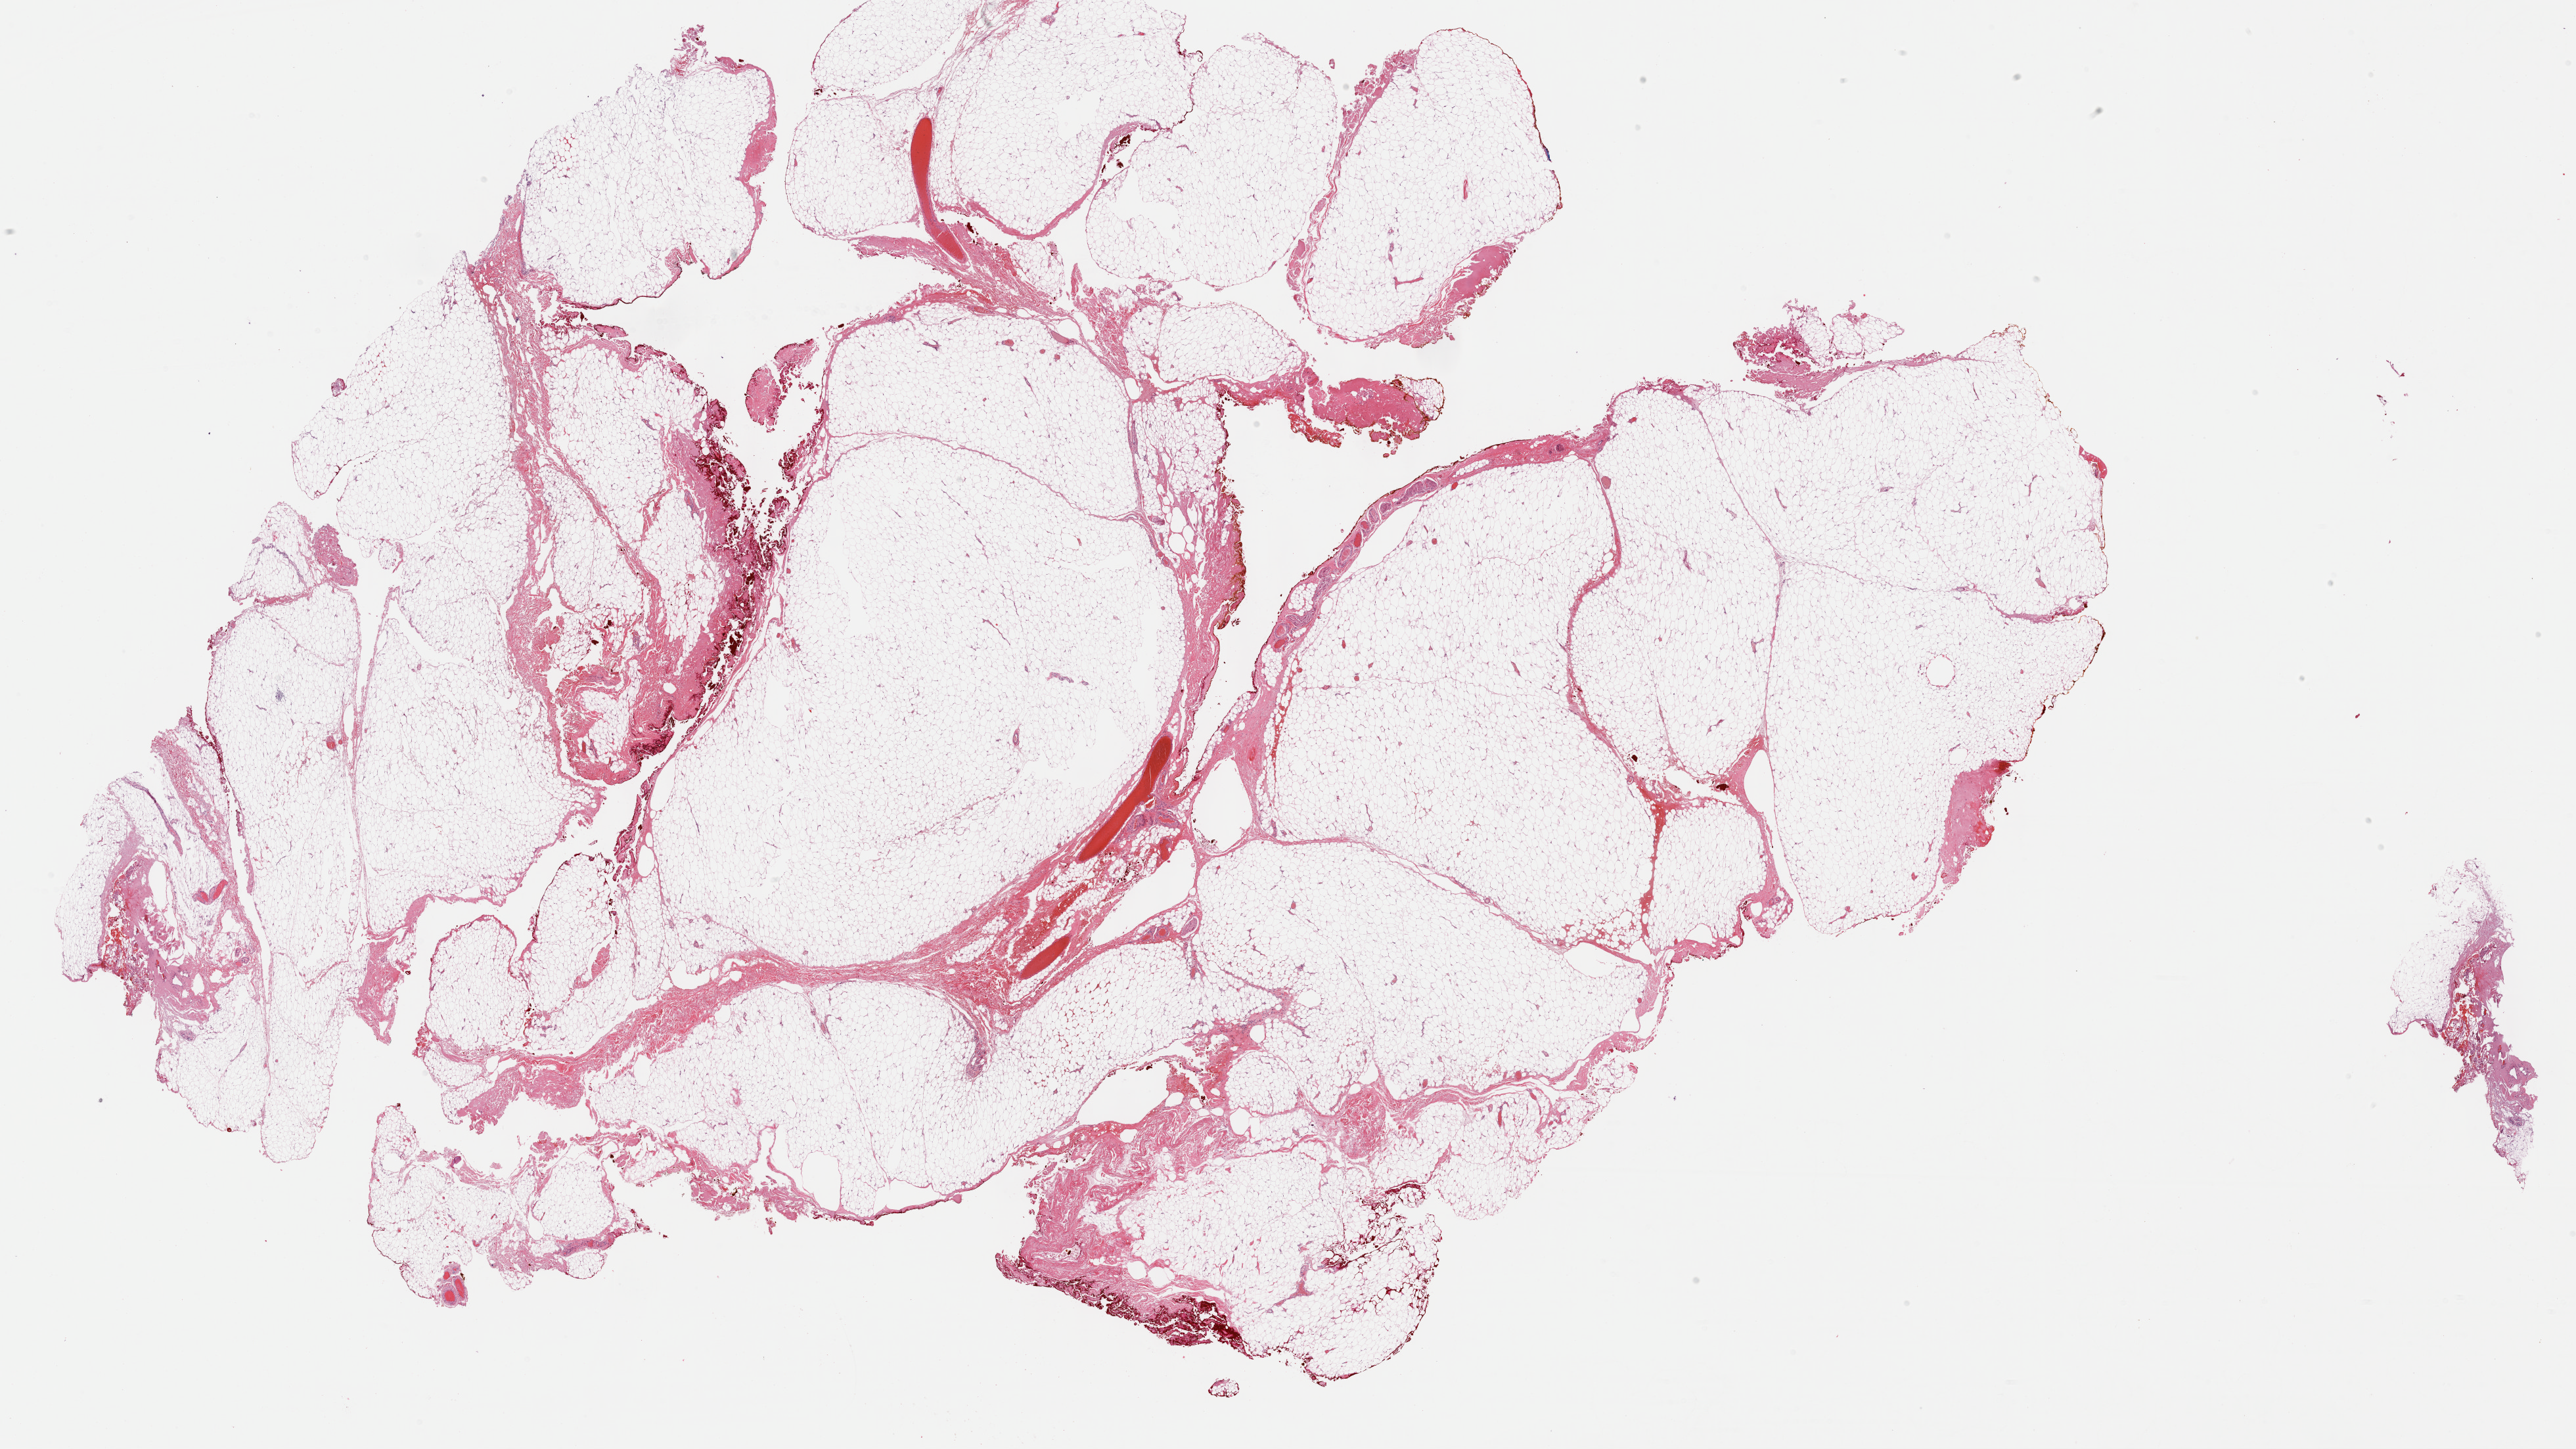
Whole-slide histology image, H&E, whole scanned area (about 31.7 x 17.8 mm, acquisition: 40x scan) shown as a low-resolution overview; formalin-fixed paraffin-embedded (FFPE) diagnostic section; primary tumour sample from the connective, subcutaneous and other soft tissues. Patient: male, age at initial diagnosis 35 years.
Histologic diagnosis: Fibromyxosarcoma (connective, subcutaneous and other soft tissues of lower limb and hip).